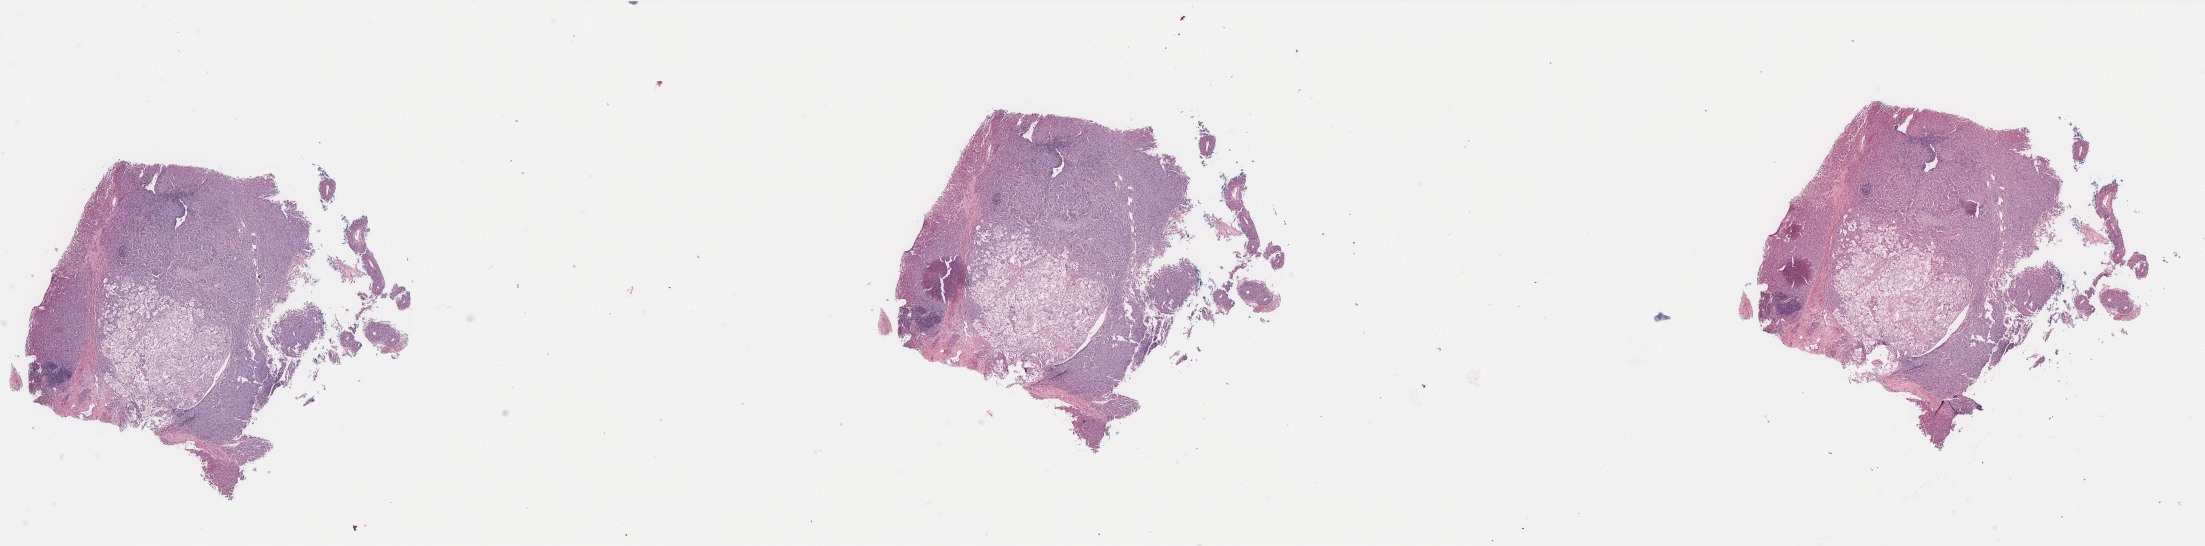
Whole-slide histology image, H&E — shown as a low-resolution overview of the whole scanned area (about 35.4 x 8.8 mm, from a 40x scan). Formalin-fixed paraffin-embedded (FFPE) diagnostic section. Primary tumour sample from the skin. Female patient; age at initial diagnosis 27 years.
Pathologic diagnosis: Malignant melanoma, NOS.